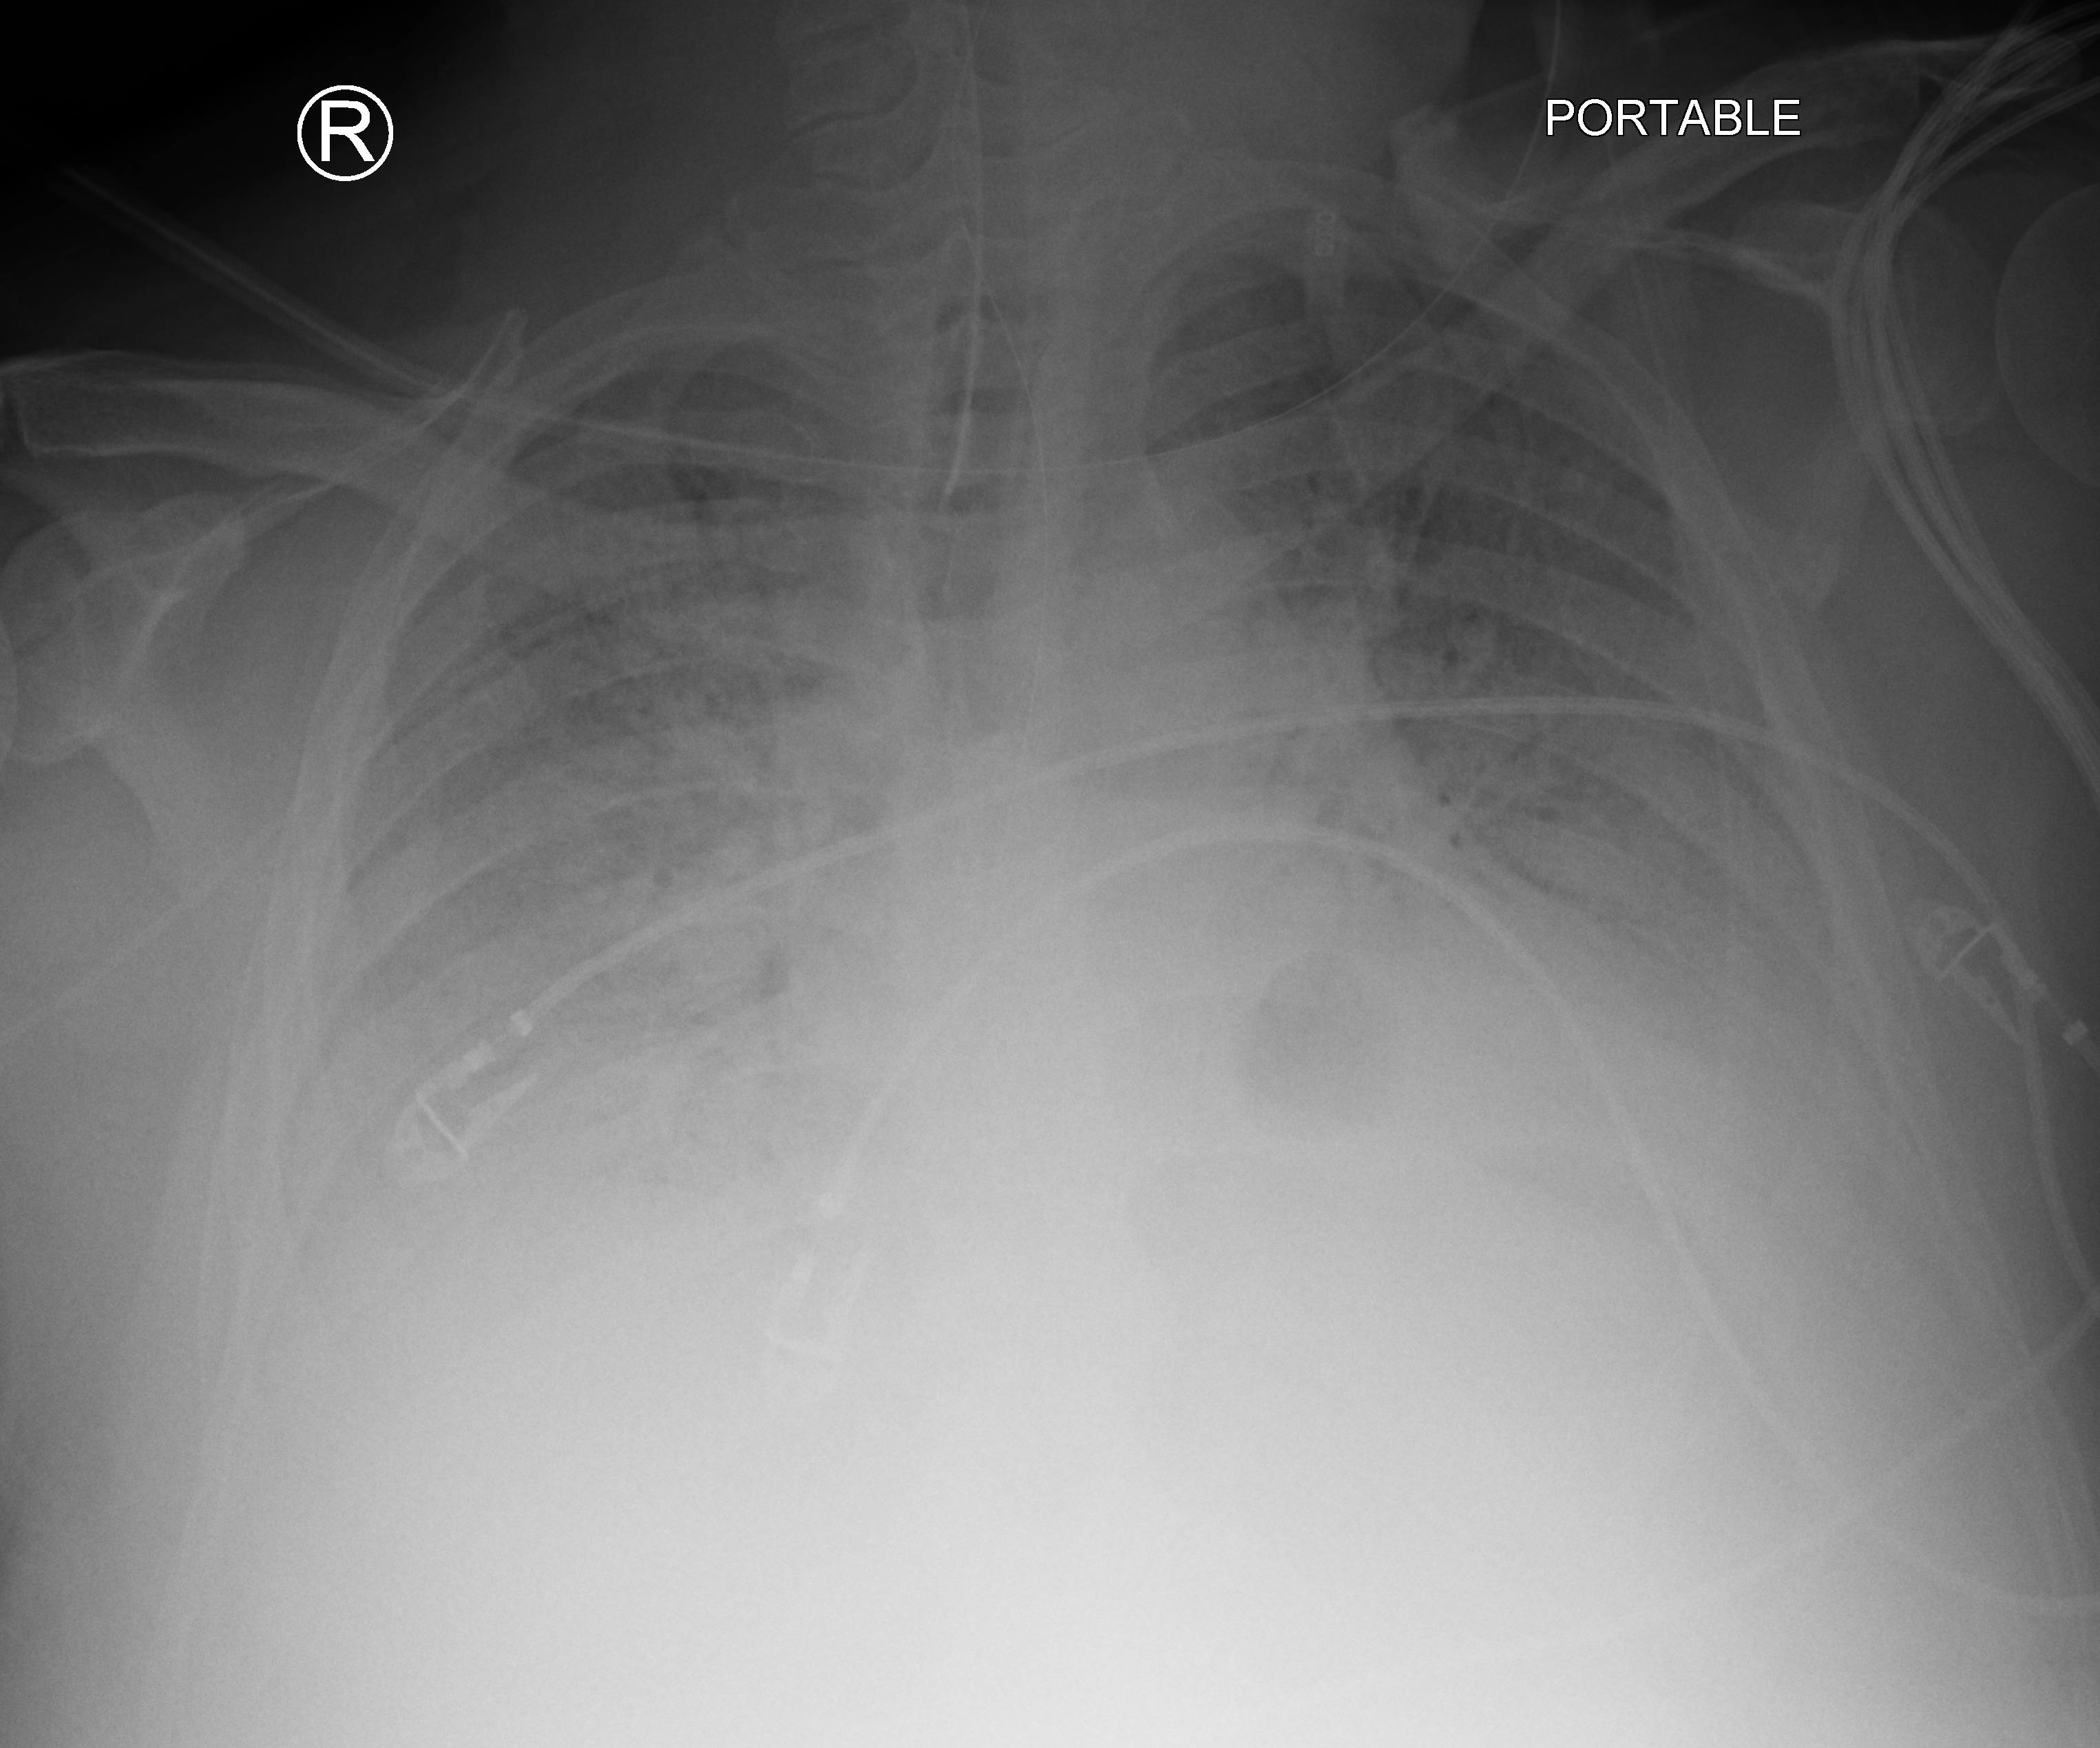
Bedside chest radiograph (computed radiography), anteroposterior (AP) projection. Adult patient hospitalised with COVID-19, age 18–59 years.
Hospital-stay facts (about this admission, not read from this image; timing relative to this image not recorded): chronic kidney disease (admission record): no.